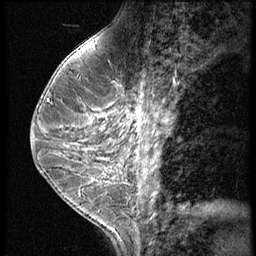
Breast MRI (dynamic contrast-enhanced), one sagittal slice; 3 images stored at this slice position (order not interpretable as contrast timing); 1.5 T; TE 4.2 ms, TR 9 ms; 256 × 256 image matrix, field of view 180 × 180 mm. Female patient, age 38 years. Case-level facts recorded for this patient, not image findings: setting: breast cancer imaged before/during neoadjuvant chemotherapy; receptor status: triple-negative.
Structures marked on this image (semi-automatic segmentation, software-assisted and operator-edited):
- analysis volume of interest (the breast-tissue region the enhancement analysis was run in; not a lesion): bounding box <119,93,165,150> (left, top, right, bottom; pixels)
- tumour enhancement mask (voxels above the 140 % enhancement threshold inside the analysis volume of interest): <121,124,137,134>